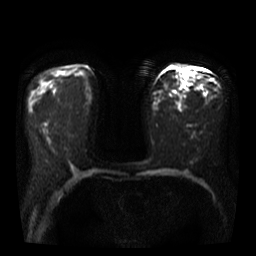
Breast MRI, one axial slice. Slice 20 of 40 in the series (ordered by position). Diffusion-weighted series; image 2 of 4 stored at this slice position (different b-values; order by instance number). 3 T. 5 mm slice thickness. 256 × 256 image matrix, field of view 360 × 360 mm. Female patient.
Outlined on this slice (manually delineated by an expert):
- tumour on diffusion-weighted imaging: bounding box <184,73,190,79> (left, top, right, bottom; pixels)